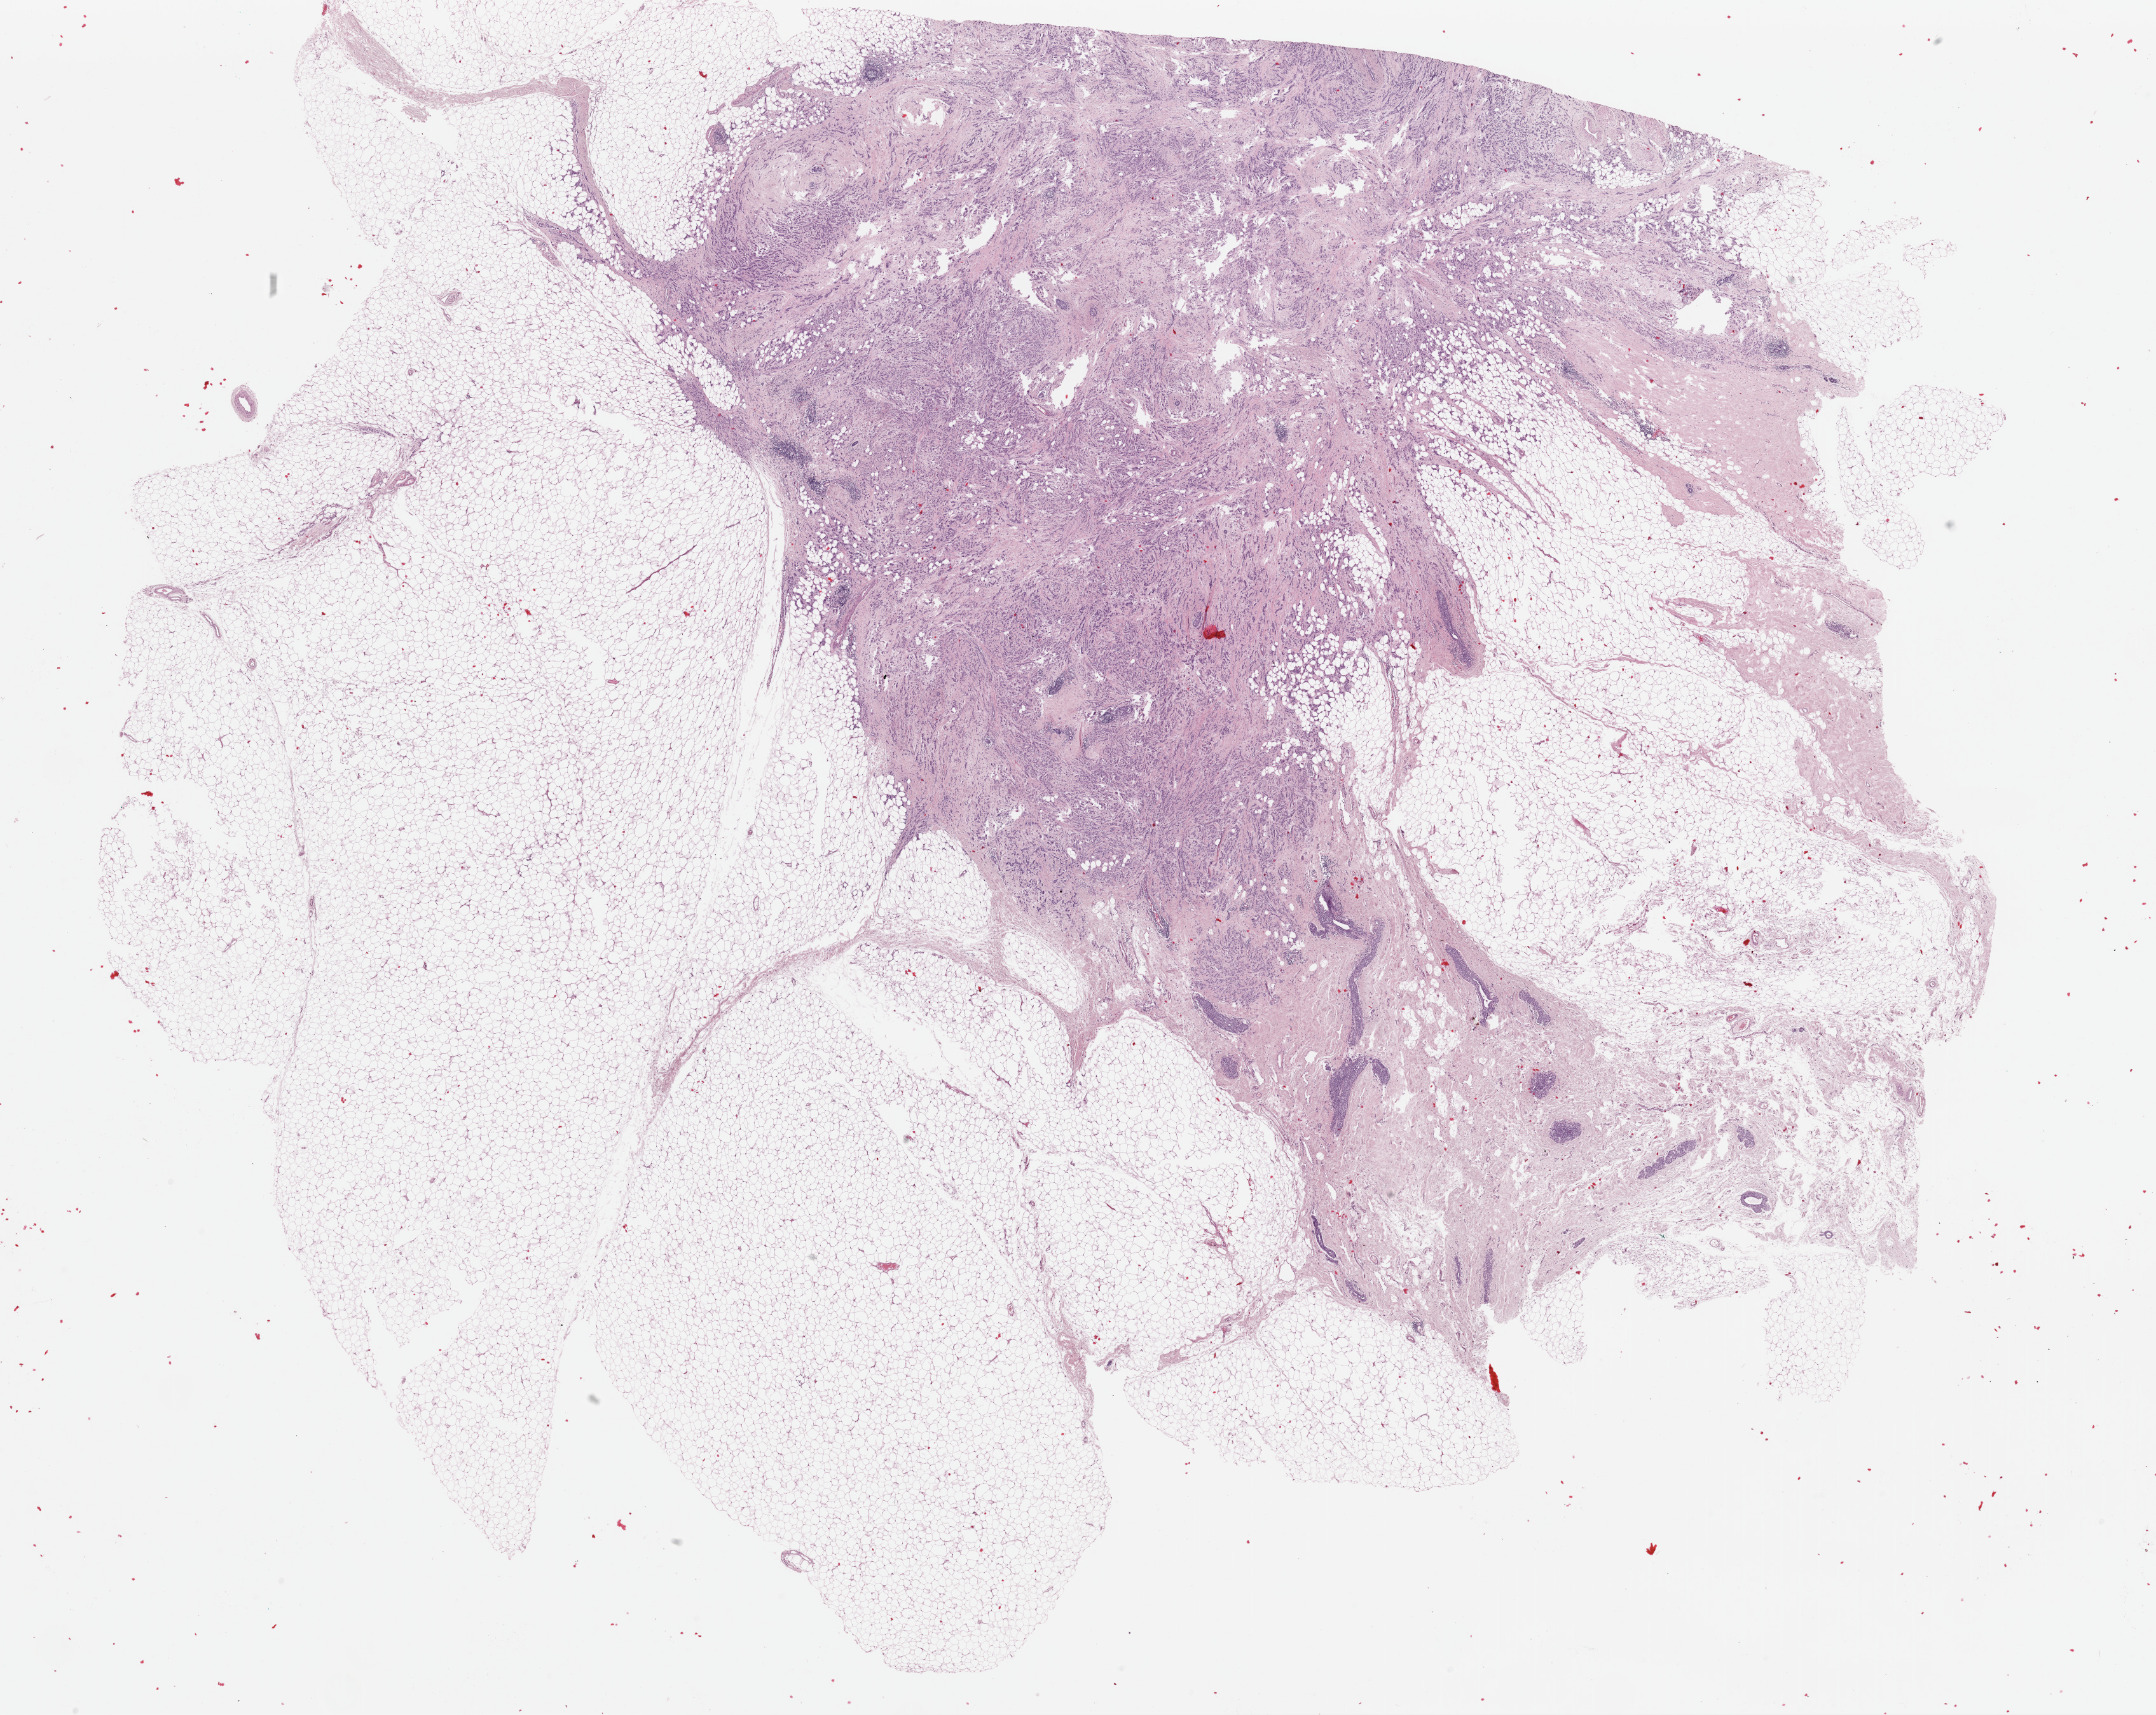
Digitized Hematoxylin and eosin (H&E) stained tissue section (whole slide) — whole scanned area (about 26.8 x 21.3 mm, slide scanned at 40x) shown as a low-resolution overview; formalin-fixed paraffin-embedded (FFPE) diagnostic section; breast, primary tumour sample. Female, age 56 years at initial diagnosis.
• lymph nodes positive (case pathology): 1 of 10 examined
• AJCC pathologic stage: IIB (7th edition)
• pathologic diagnosis: Lobular carcinoma, NOS